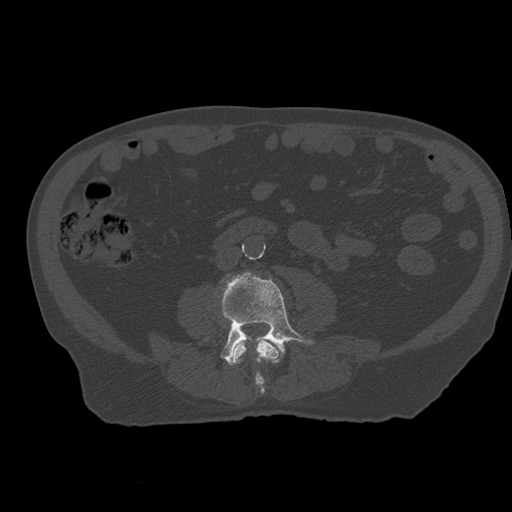
CT including the spine, one axial slice; 120 kVp; bone window (W 1800 / L 400 HU); 1.25 mm slice thickness; 512 × 512 image matrix, field of view 407 × 407 mm. Patient age 73 years. Case-level facts recorded for this patient, not image findings: primary cancer: prostate.
Structures marked on this image (semi-automatically segmented with operator editing):
- L3 vertebra: bounding box (x1, y1, x2, y2) in pixels: (232, 339, 280, 394)
- L4 vertebra: (221, 272, 314, 365)